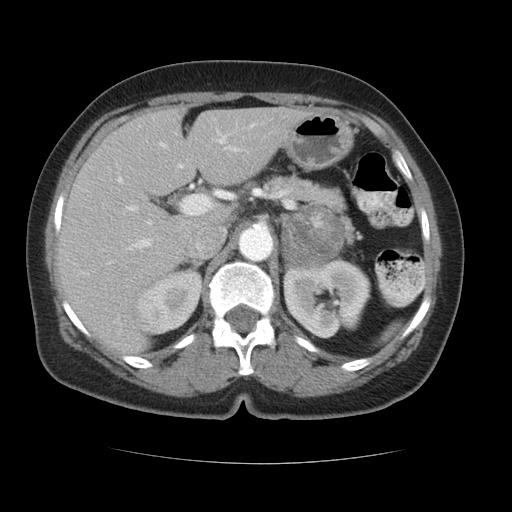
Contrast-enhanced abdominal CT, one axial slice. Position 67 of 96 along the scan axis. Reconstruction kernel STANDARD. 120 kVp. Intravenous contrast given. Soft-tissue window (W 400 / L 40 HU). 5 mm slice thickness. 512 × 512 image matrix, field of view 348 × 348 mm. Female patient, age 66 years. Case-level facts recorded for this patient, not image findings: diagnosis: adrenocortical carcinoma; tumour side: left adrenal; tumour size at pathology: 5.5 cm; Ki-67 index: 15 %; stage (as recorded): 3.
Structures marked on this image (semi-automatic segmentation, software-assisted and operator-edited):
- mass: bounding box <283,206,343,266> (left, top, right, bottom; pixels)